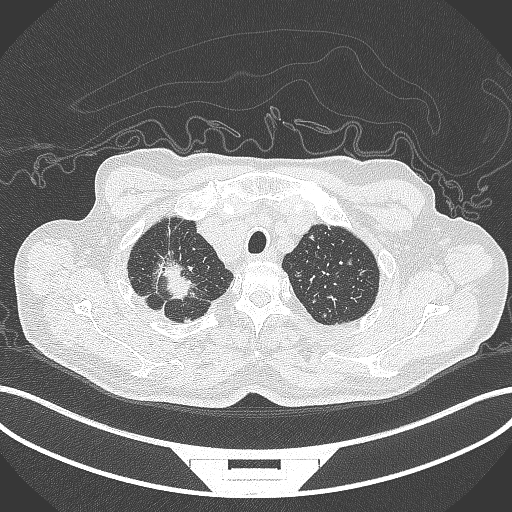
Chest CT, one axial slice. Slice 338 of 407 in the series (ordered by position). Reconstruction kernel B70f. 120 kVp. Lung window (W 1500 / L -600 HU). 1 mm slice thickness. 512 × 512 image matrix. Male patient, age 69 years. Case-level facts recorded for this patient, not image findings: clinical TNM (as recorded): T1c N1 M1.
Annotated regions visible in this slice (bounding box drawn by a radiologist):
- lung tumour (recorded histology: adenocarcinoma): bounding box <149,250,205,302> (left, top, right, bottom; pixels)